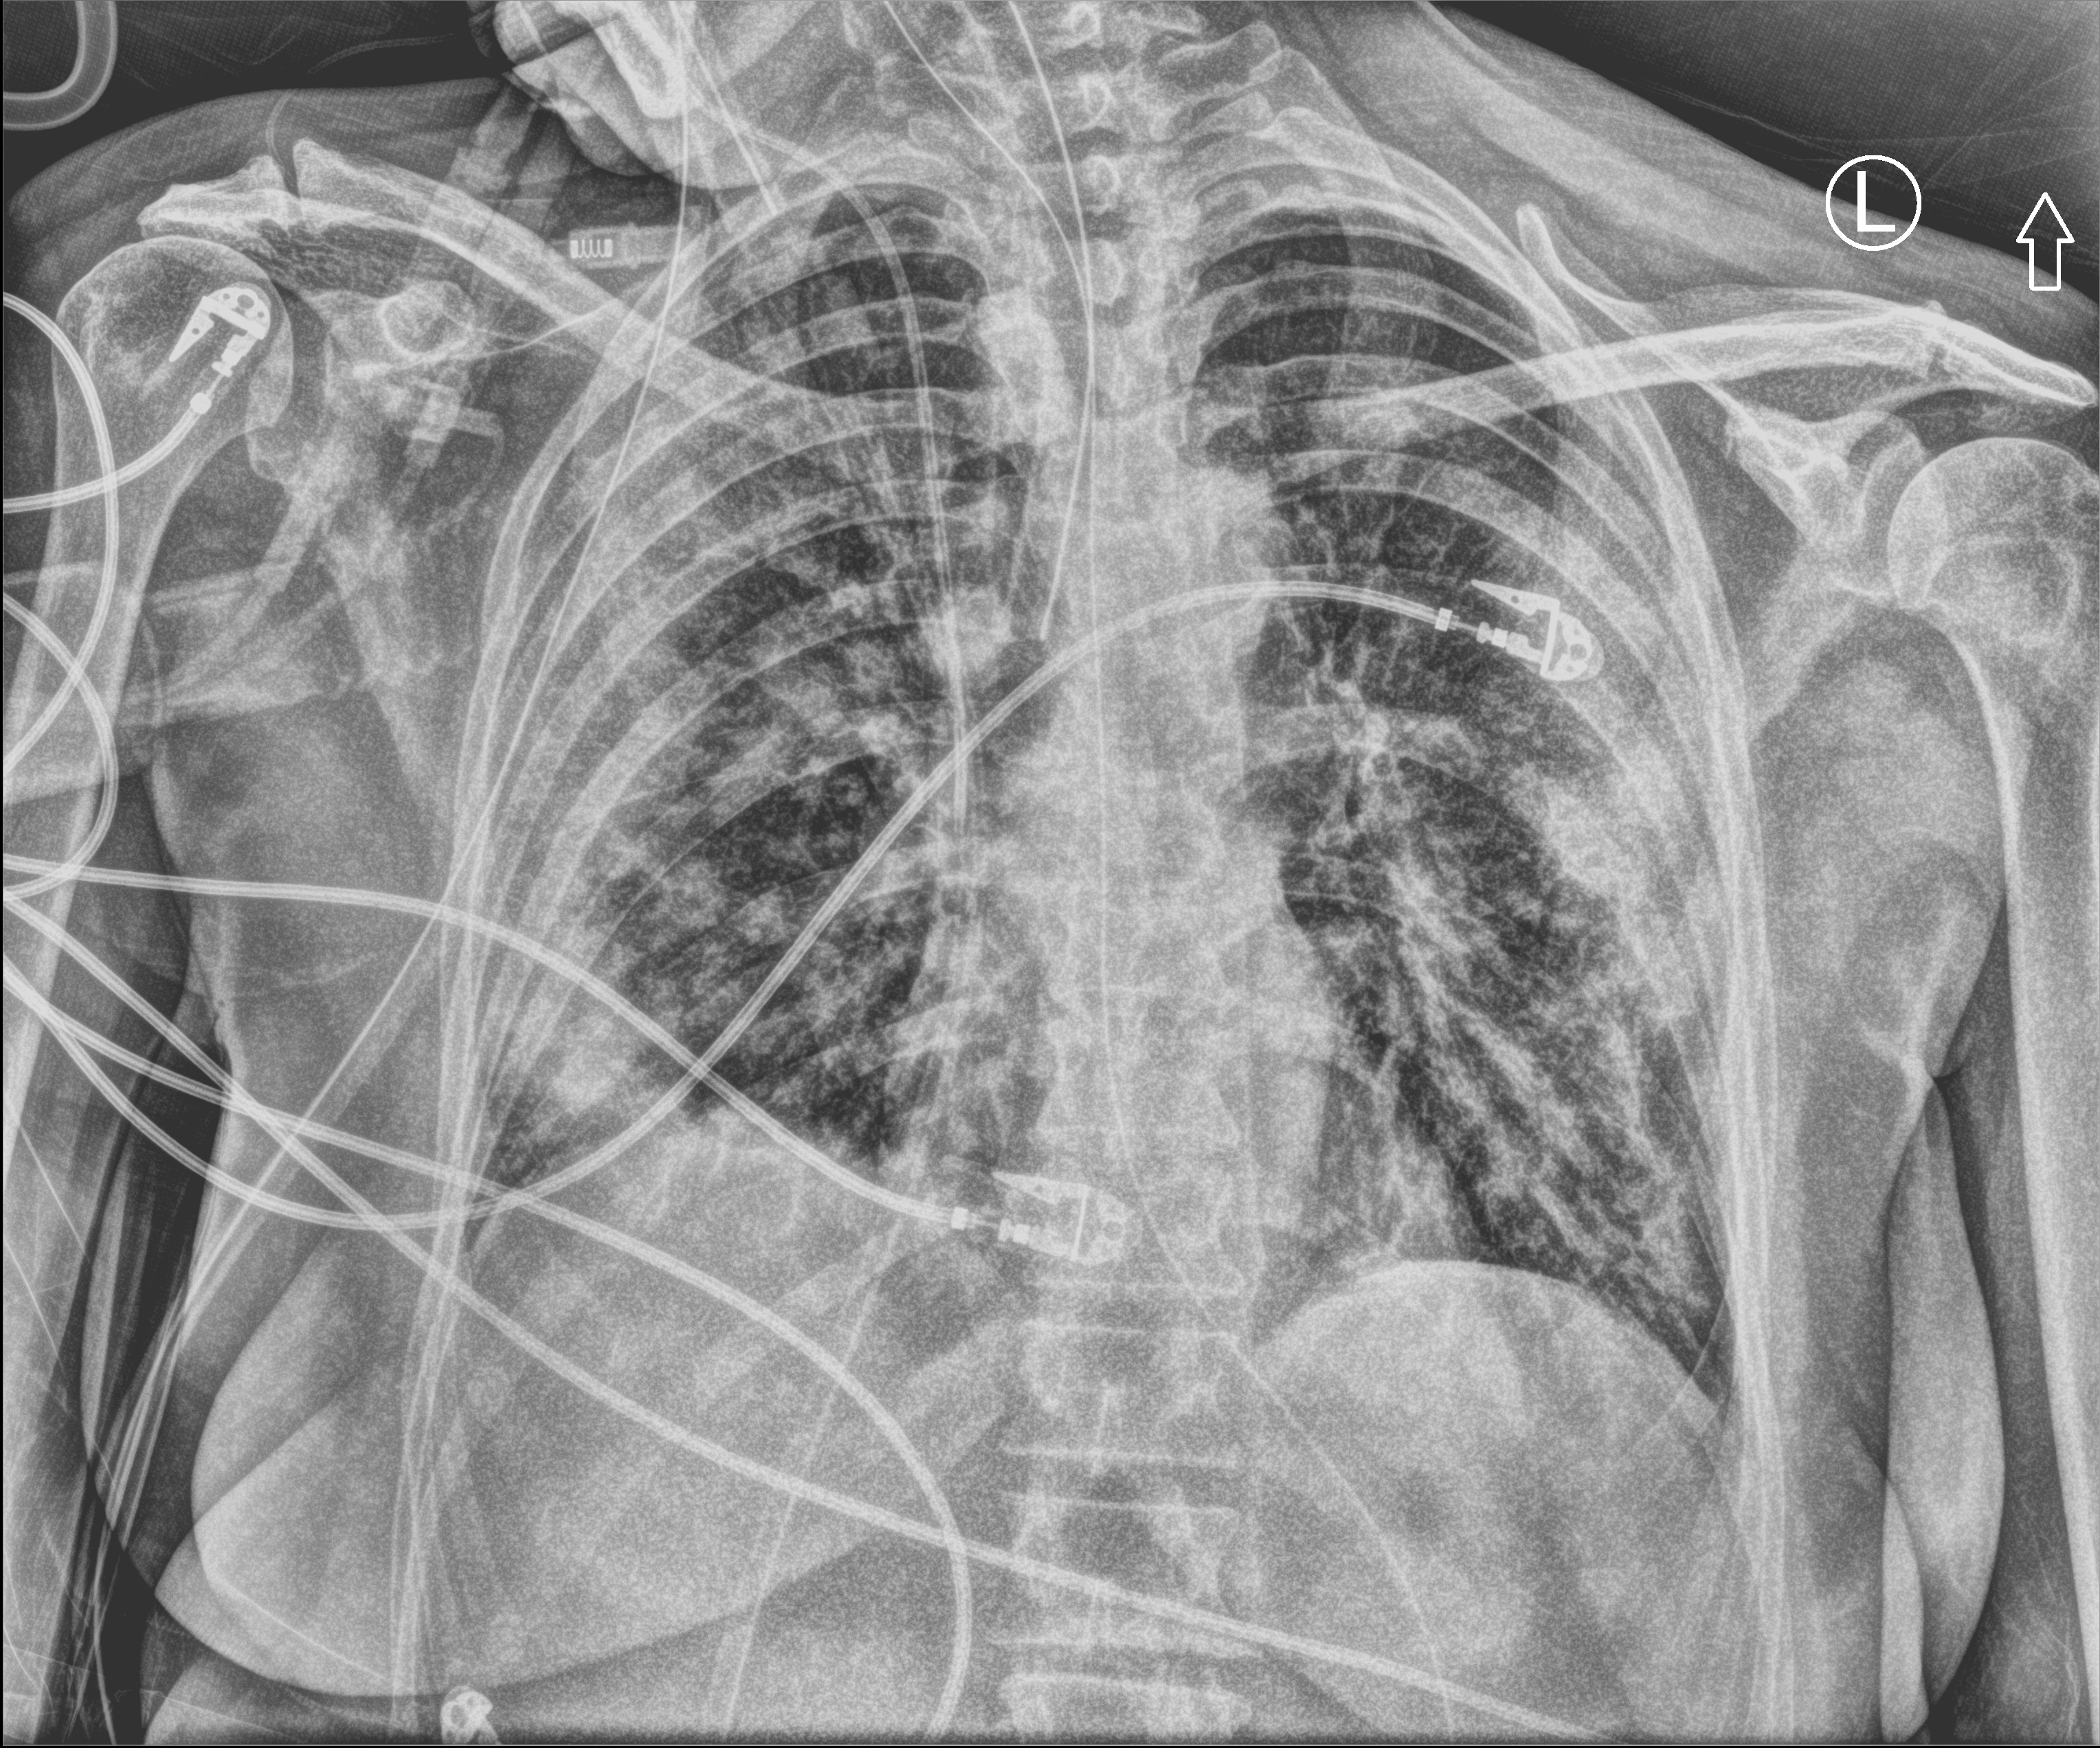
Bedside chest radiograph (computed radiography), anteroposterior (AP) projection. Female patient hospitalised with COVID-19, age 60–74 years.
From the hospital-stay record, not from the radiograph (when in the stay this image was taken is not recorded): hypertension (admission record): yes.